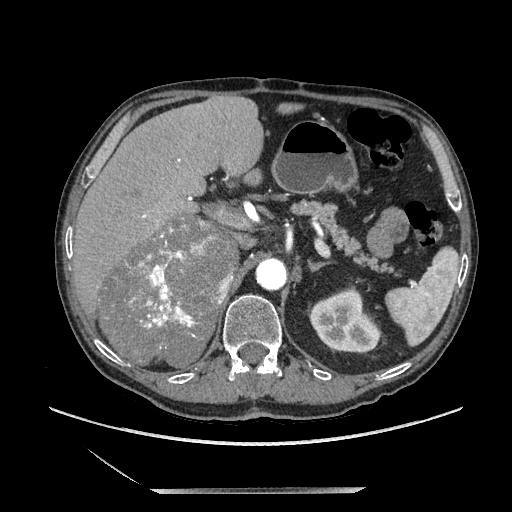
Contrast-enhanced abdominal CT, one axial slice. Slice 134 of 243 in the series (ordered by position). Soft-tissue window (W 400 / L 40 HU). 512 × 512 image matrix, field of view 420 × 420 mm. Male patient. Case-level facts recorded for this patient, not image findings: diagnosis: adrenocortical carcinoma; tumour side: right adrenal; tumour size at pathology: 16 cm; Ki-67 index: 17 %; stage (as recorded): 3.
Annotated regions visible in this slice (semi-automatically segmented with operator editing):
- mass: bounding box <101,217,238,367> (left, top, right, bottom; pixels)